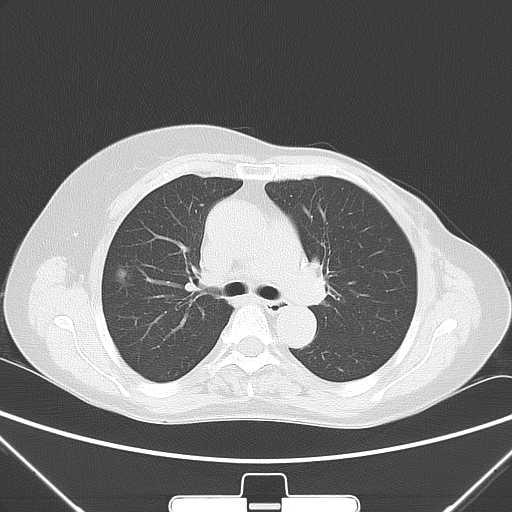
Chest CT, one axial slice; position 33 of 53 along the scan axis; 120 kVp; lung window (W 1500 / L -600 HU); 512 × 512 image matrix, field of view 350 × 350 mm. Patient: female, 64 years. From the clinical record (not read from this slice): clinical TNM (as recorded): T1c N0 M0; histopathological grade: G1-2.
Structures marked on this image (bounding box drawn by a radiologist):
- lung tumour (recorded histology: adenocarcinoma): box from (x=110, y=260) to (x=130, y=287) px